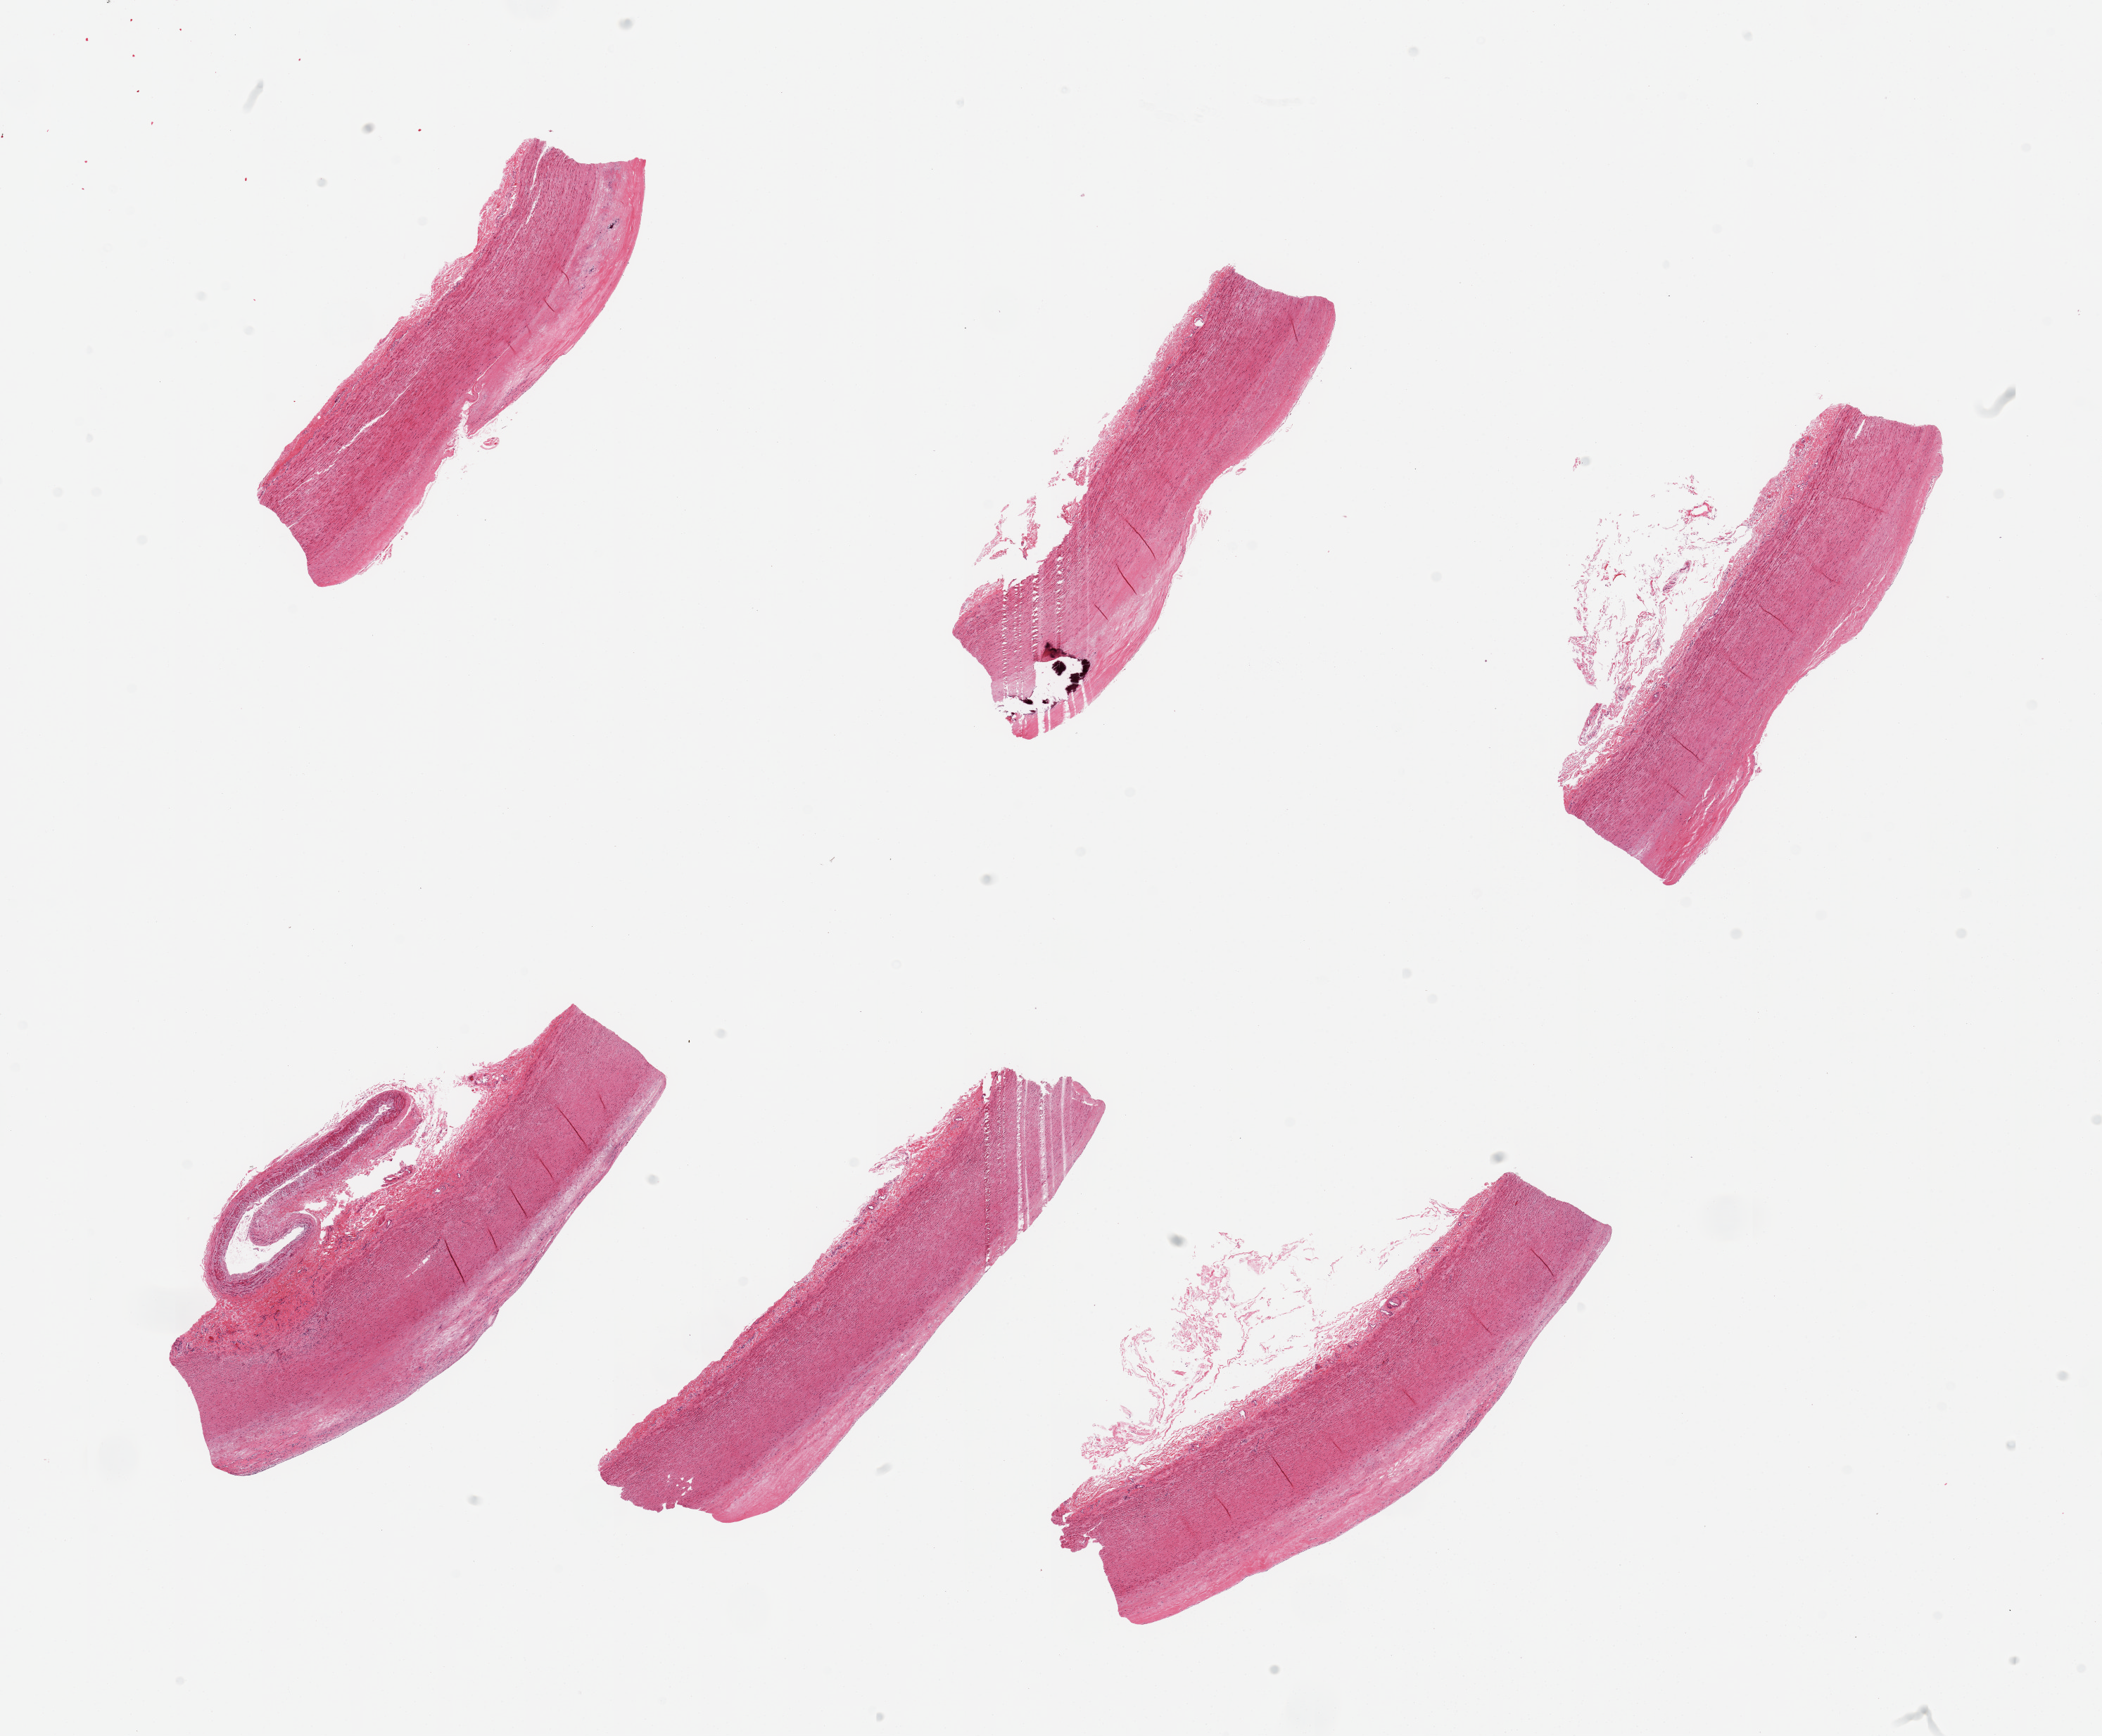
Hematoxylin and eosin (H&E) whole-slide image, a low-resolution overview of the entire scanned area, about 23.6 x 19.5 mm; PAXgene-fixed paraffin-embedded (PFPE) section; sampled site (target tissue): aorta; tissue donor sample. Male donor.
- review note (as recorded): 6 pieces, atherosis up to ~0.6